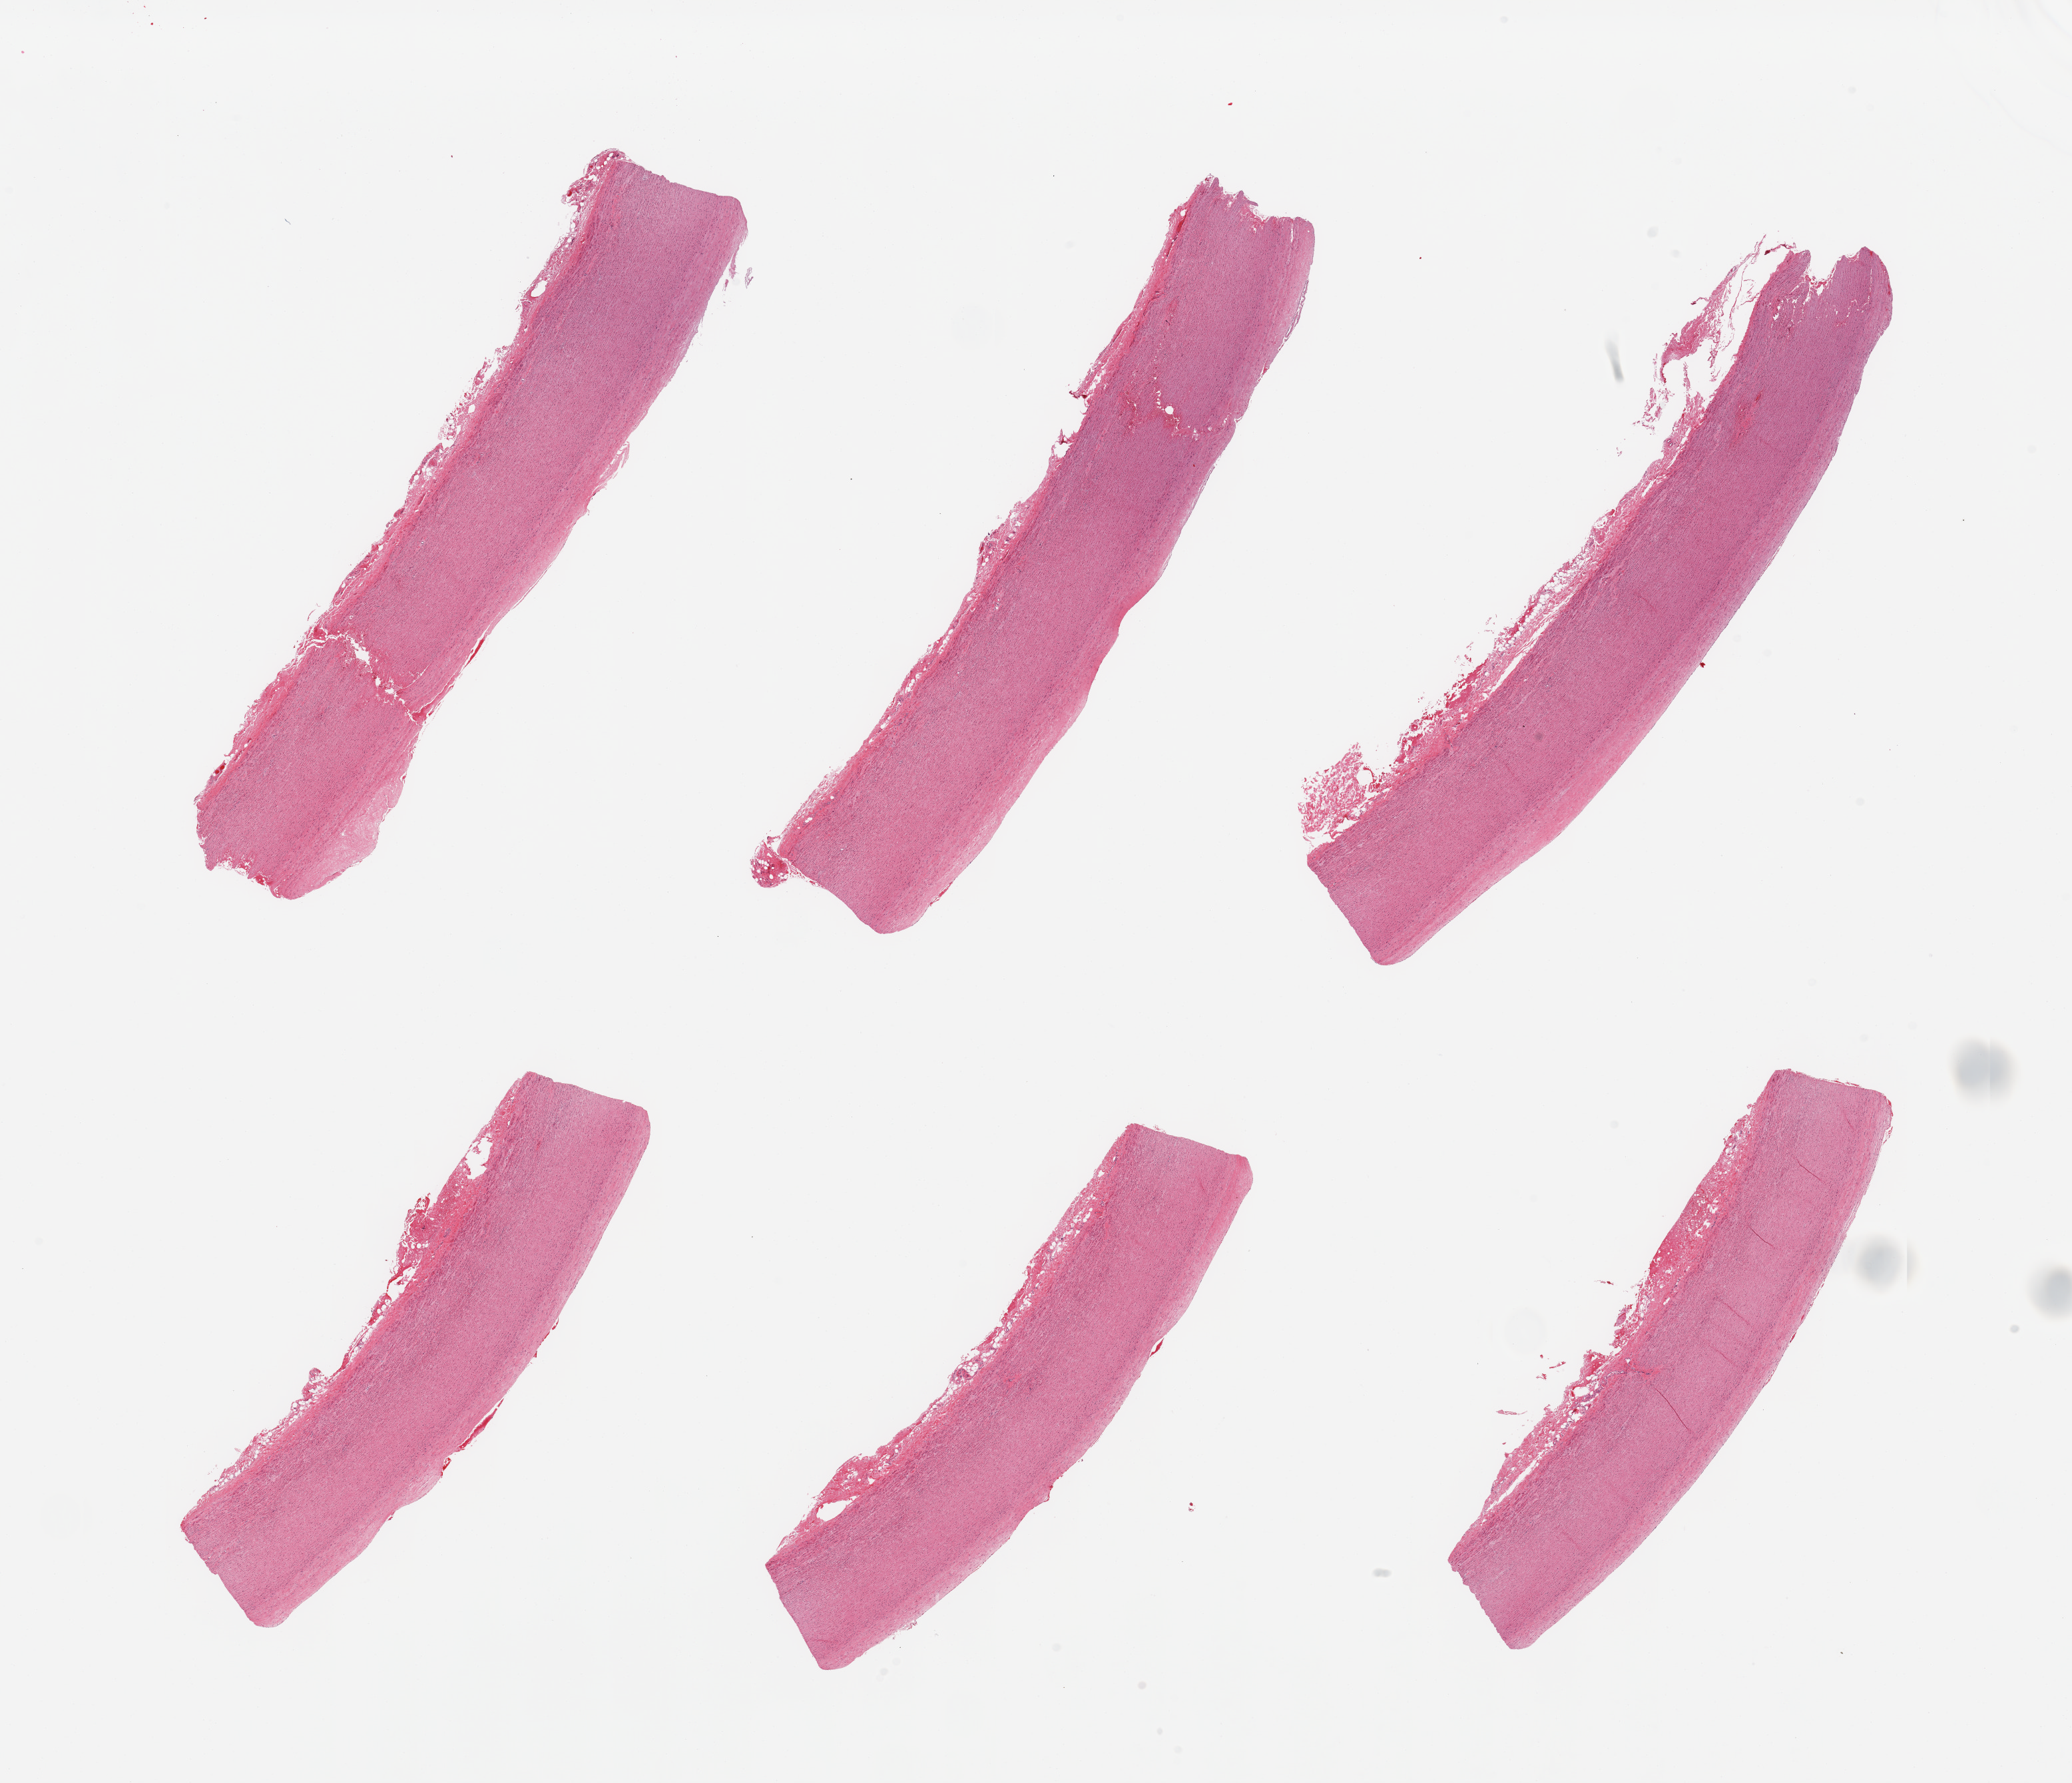
Digitized hematoxylin and eosin (H&E)-stained section — whole scanned area (about 24.6 x 21.2 mm, from a 20x scan) shown as a low-resolution overview; PAXgene-fixed, paraffin-embedded tissue; sampled site (target tissue): aorta; donor tissue sample. Male donor.
Review note (as recorded): 6 pieces; mild flat plaques; well trimmed.